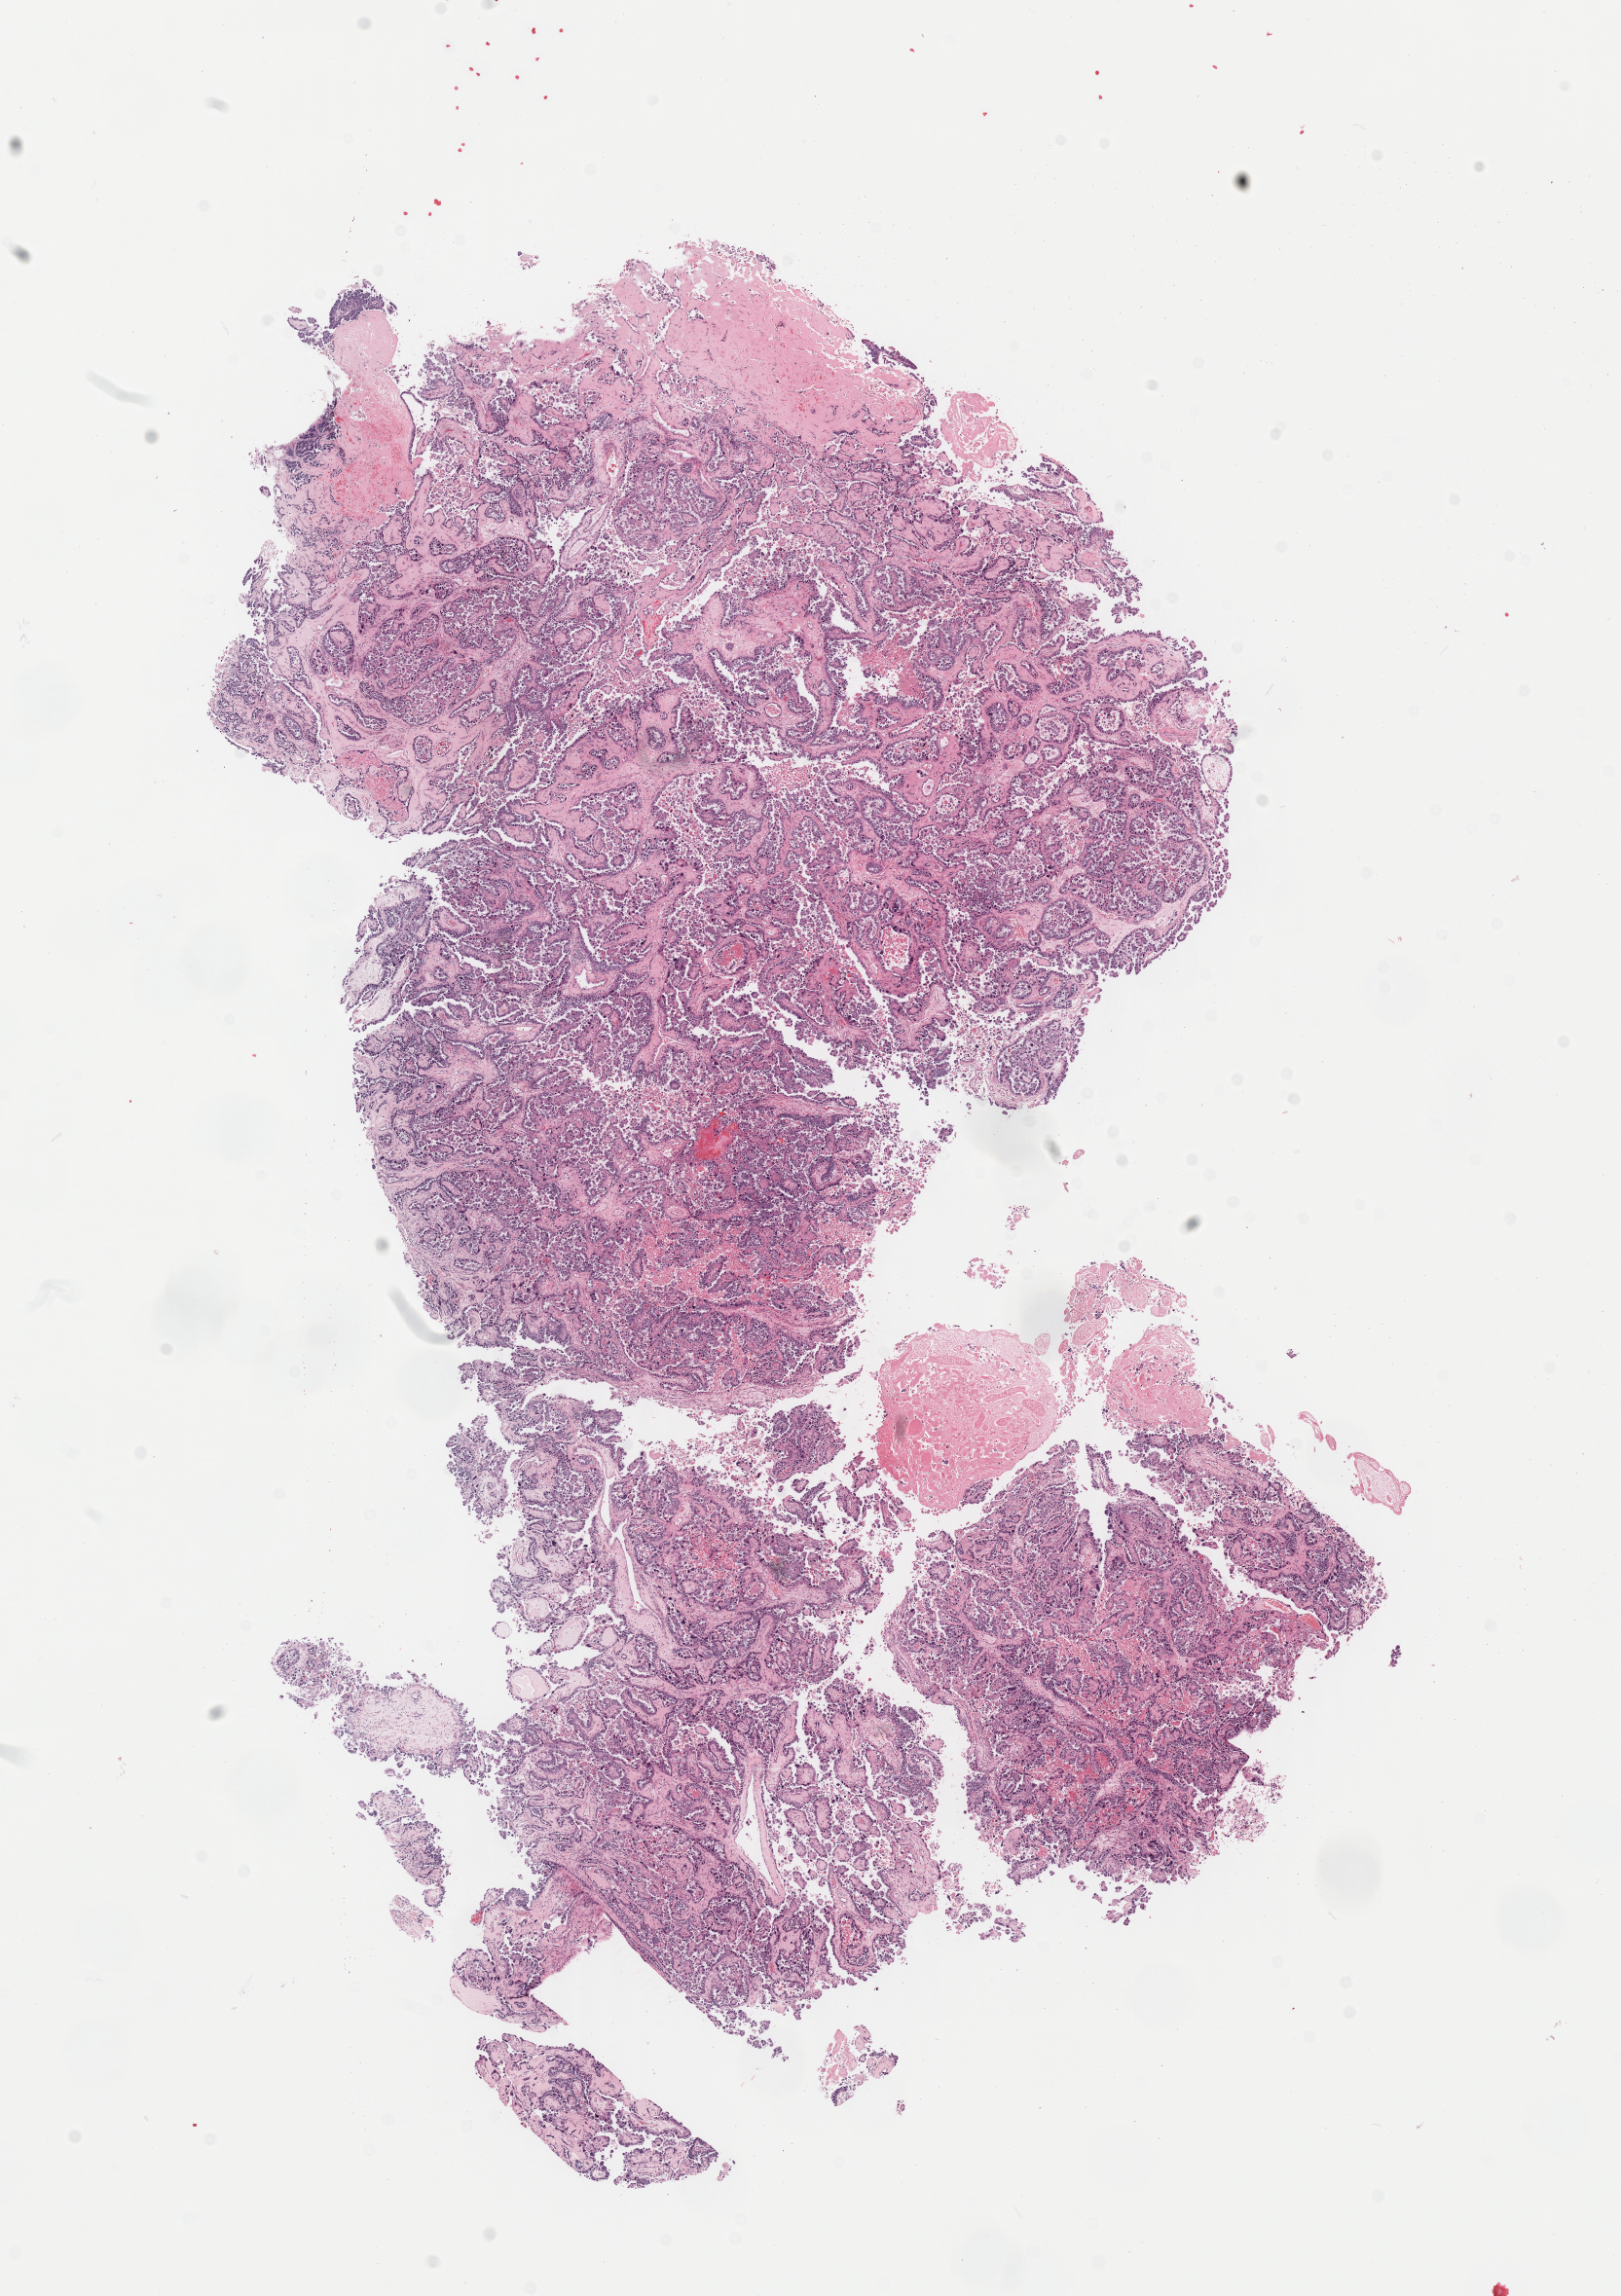
Digitized H&E-stained tissue section (whole slide), low-resolution overview of the scanned area, about 13.2 x 18.7 mm; formalin-fixed paraffin-embedded (FFPE) diagnostic section; sample: primary tumour, uterus. Patient: female, age at initial diagnosis 61 years.
Pathologic diagnosis: Serous cystadenocarcinoma, NOS.